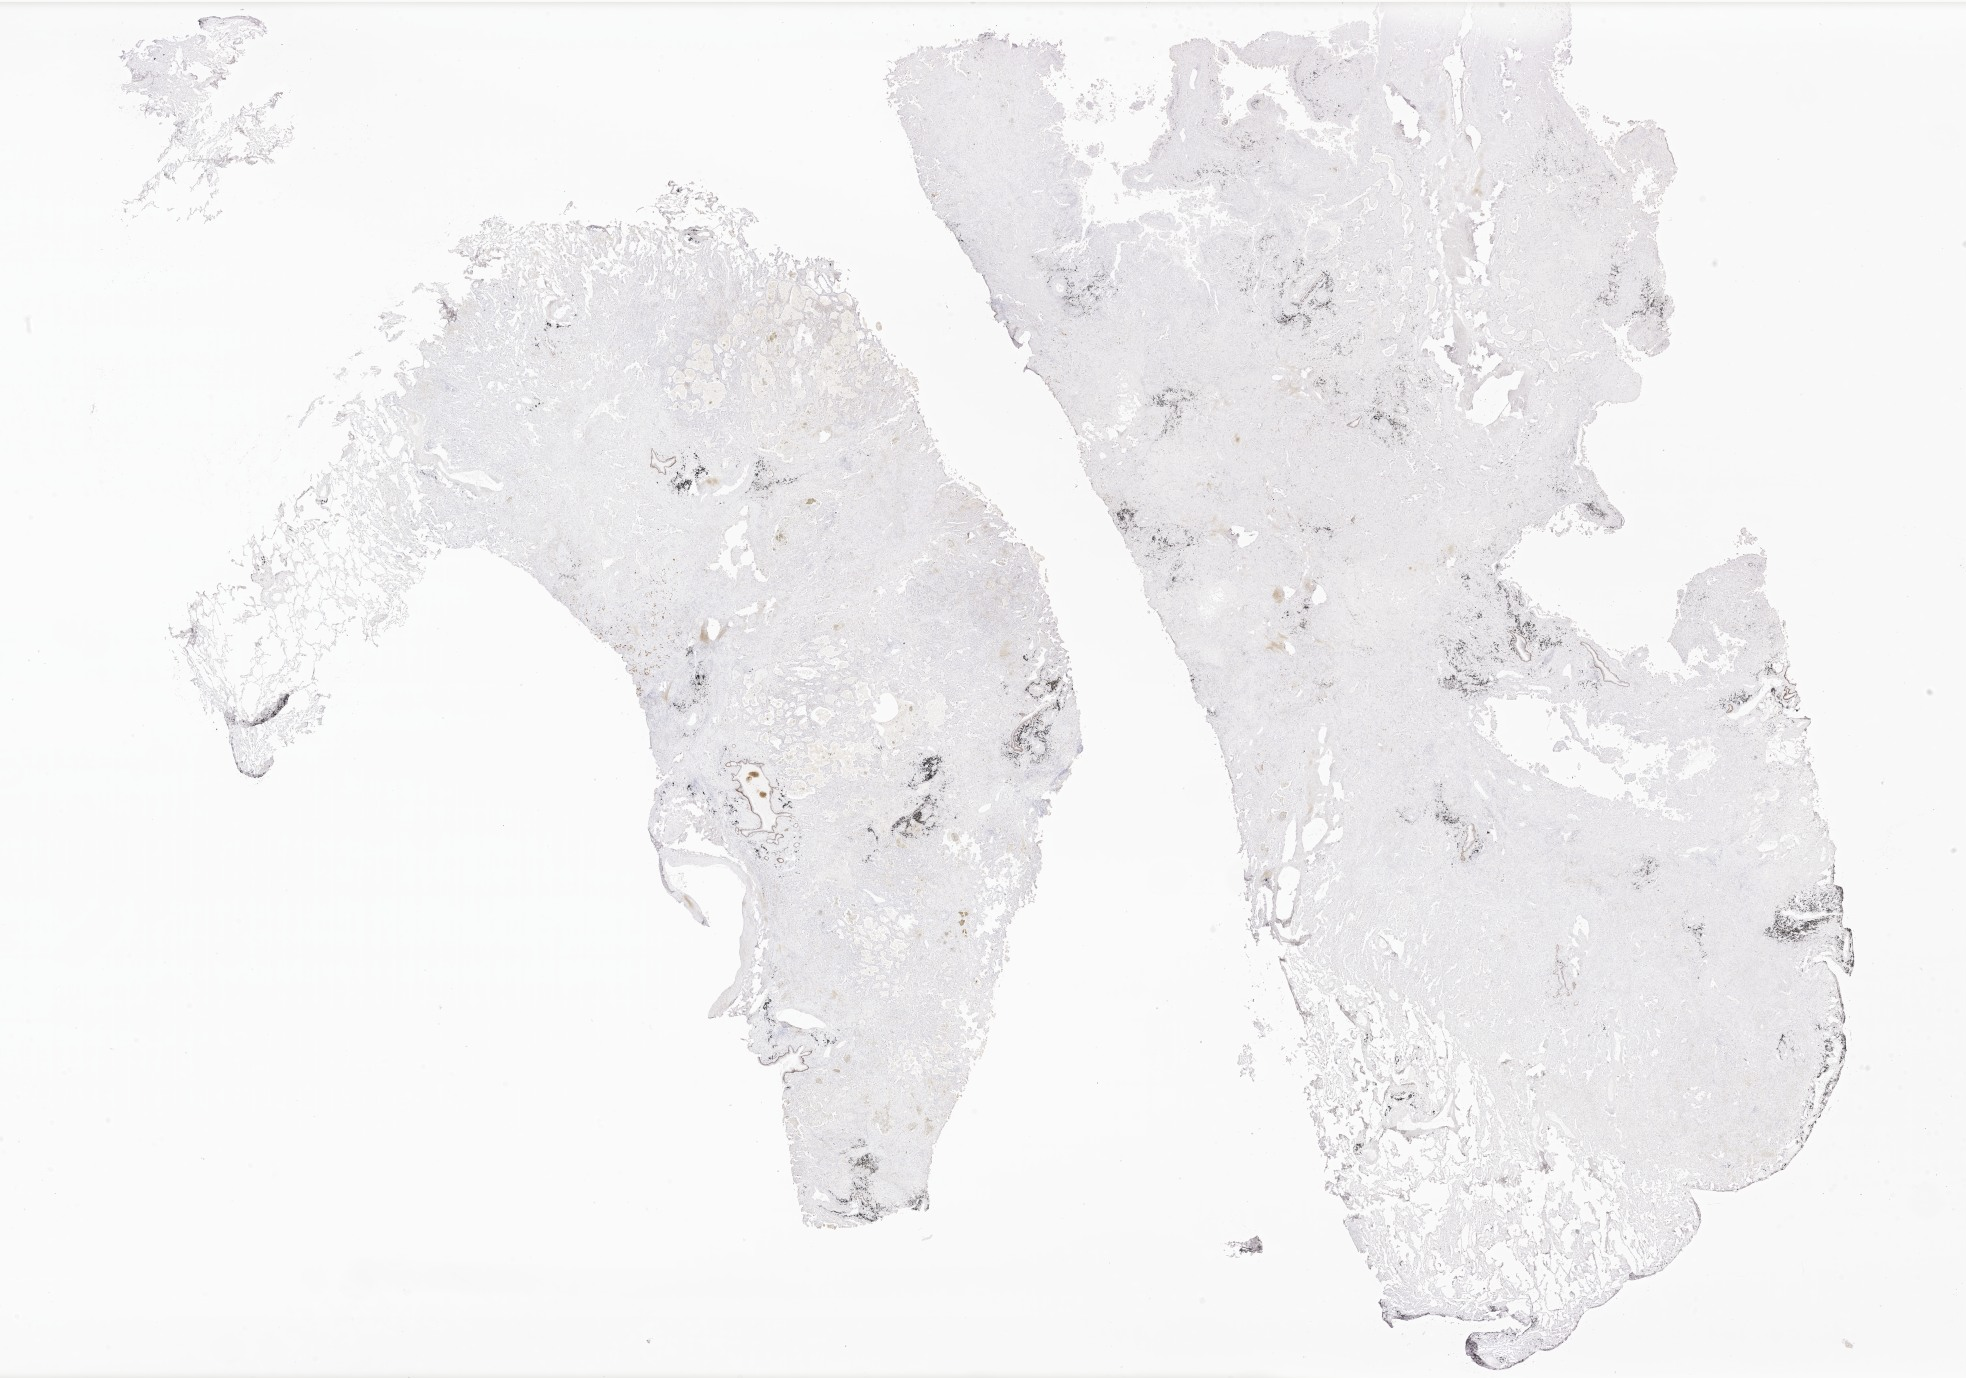
Immunohistochemistry (IHC) whole-slide image stained for p40 — a low-resolution overview of the entire scanned area, about 33.2 x 23.2 mm; tumor tissue; site: lung (right). Patient: male, age 69 years.
- diagnosis: Non-small cell carcinoma